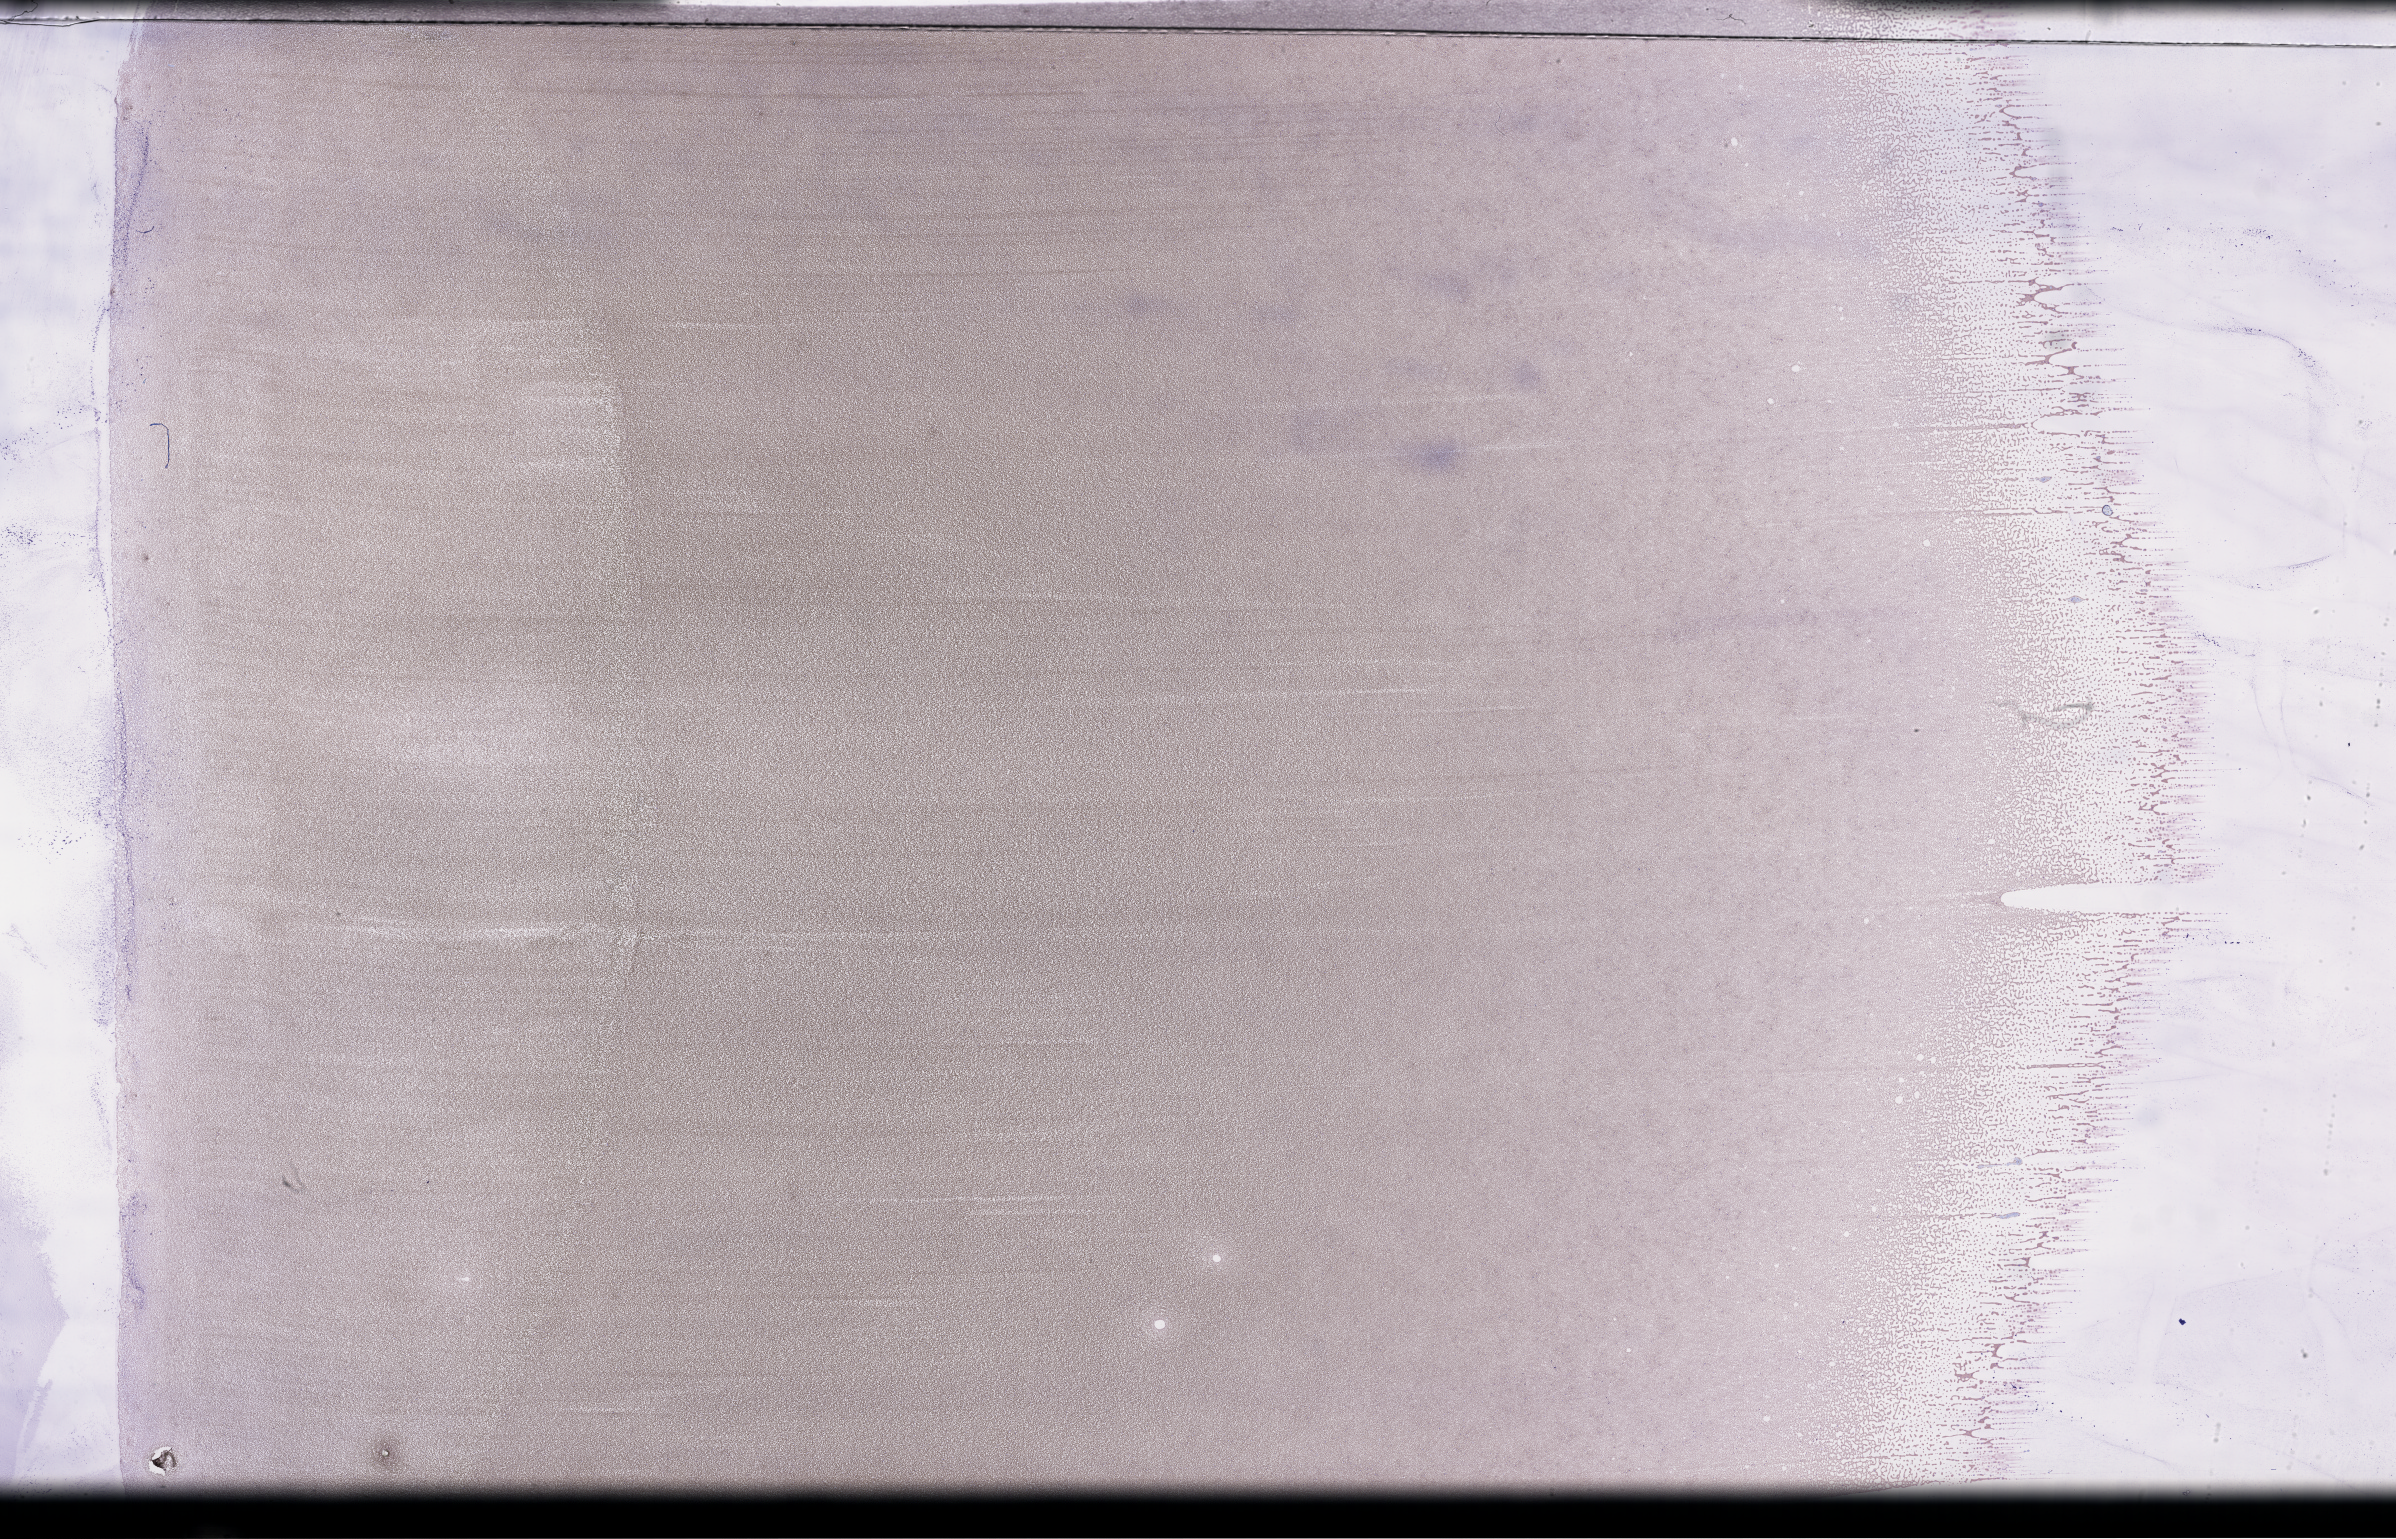
Whole-slide image of a whole blood smear, Wright-Giemsa stain, low-resolution overview of the scanned area, about 38.7 x 24.9 mm. Patient sex: female.
- patient diagnosis: Plasma Cell Myeloma